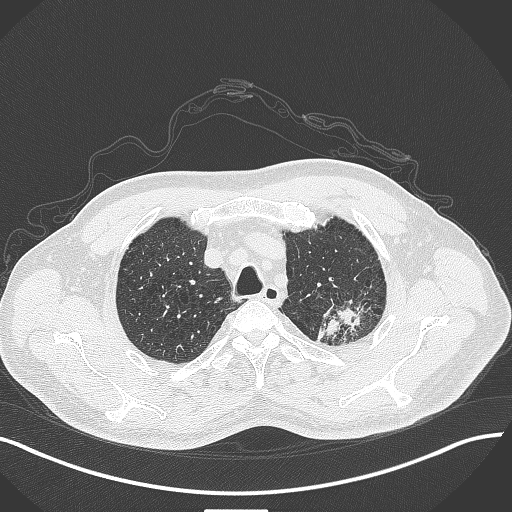
Chest CT, one axial slice. Slice 353 of 429 in the series (ordered by position). Reconstruction kernel B70f. 120 kVp. Lung window (W 1500 / L -600 HU). 1 mm slice thickness. 512 × 512 image matrix, field of view 400 × 400 mm. Male patient, age 55 years. Case-level facts recorded for this patient, not image findings: clinical TNM (as recorded): T3 N0 M1c; histopathological grade: G3.
Outlined on this slice (bounding box drawn by a radiologist):
- lung tumour (recorded histology: adenocarcinoma): box from (x=319, y=294) to (x=380, y=353) px